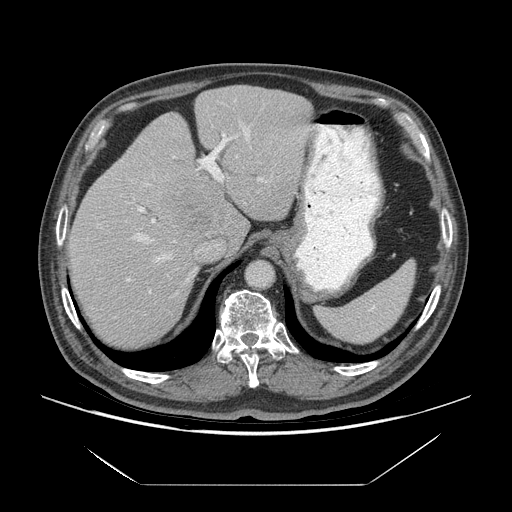
Contrast-enhanced abdominal CT (liver protocol), one axial slice. Position 50 of 75 along the scan axis. Reconstruction kernel STANDARD. Soft-tissue window (W 400 / L 40 HU). 2.5 mm slice thickness. 512 × 512 image matrix. From the clinical record (not read from this slice): diagnosis: hepatocellular carcinoma (patient treated with transarterial chemoembolisation; whether this scan precedes or follows treatment is not stated here); TNM stage (as recorded): Stage-I; Child-Pugh class: A; tumour size: 5.8 cm.
Annotated regions visible in this slice (semi-automatically segmented with operator editing):
- liver parenchyma outside the tumour (the mass and vessels are separate outlines, so this box may not span the whole liver): box from (x=68, y=84) to (x=312, y=346) px
- mass: (x=173, y=179)–(x=230, y=238)
- liver vessels: (x=127, y=100)–(x=268, y=293)